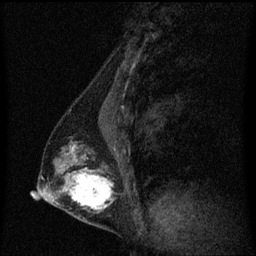
Breast MRI (dynamic contrast-enhanced), one sagittal slice; position 28 of 60 along the scan axis; dynamic contrast-enhanced series, image 2 of 3 at this slice position (ordered by acquisition); 1.5 T; TE 4.2 ms, TR 8.4 ms; 256 × 256 image matrix. Patient: female, 40 years. From the clinical record (not read from this slice): setting: breast cancer imaged before/during neoadjuvant chemotherapy; receptor status: triple-negative.
Annotated regions visible in this slice (semi-automatically segmented with operator editing):
- analysis volume of interest (the breast-tissue region the enhancement analysis was run in; not a lesion): box from (x=44, y=128) to (x=117, y=221) px
- tumour enhancement mask (voxels above the 70 % enhancement threshold inside the analysis volume of interest): (x=66, y=146)–(x=113, y=211)